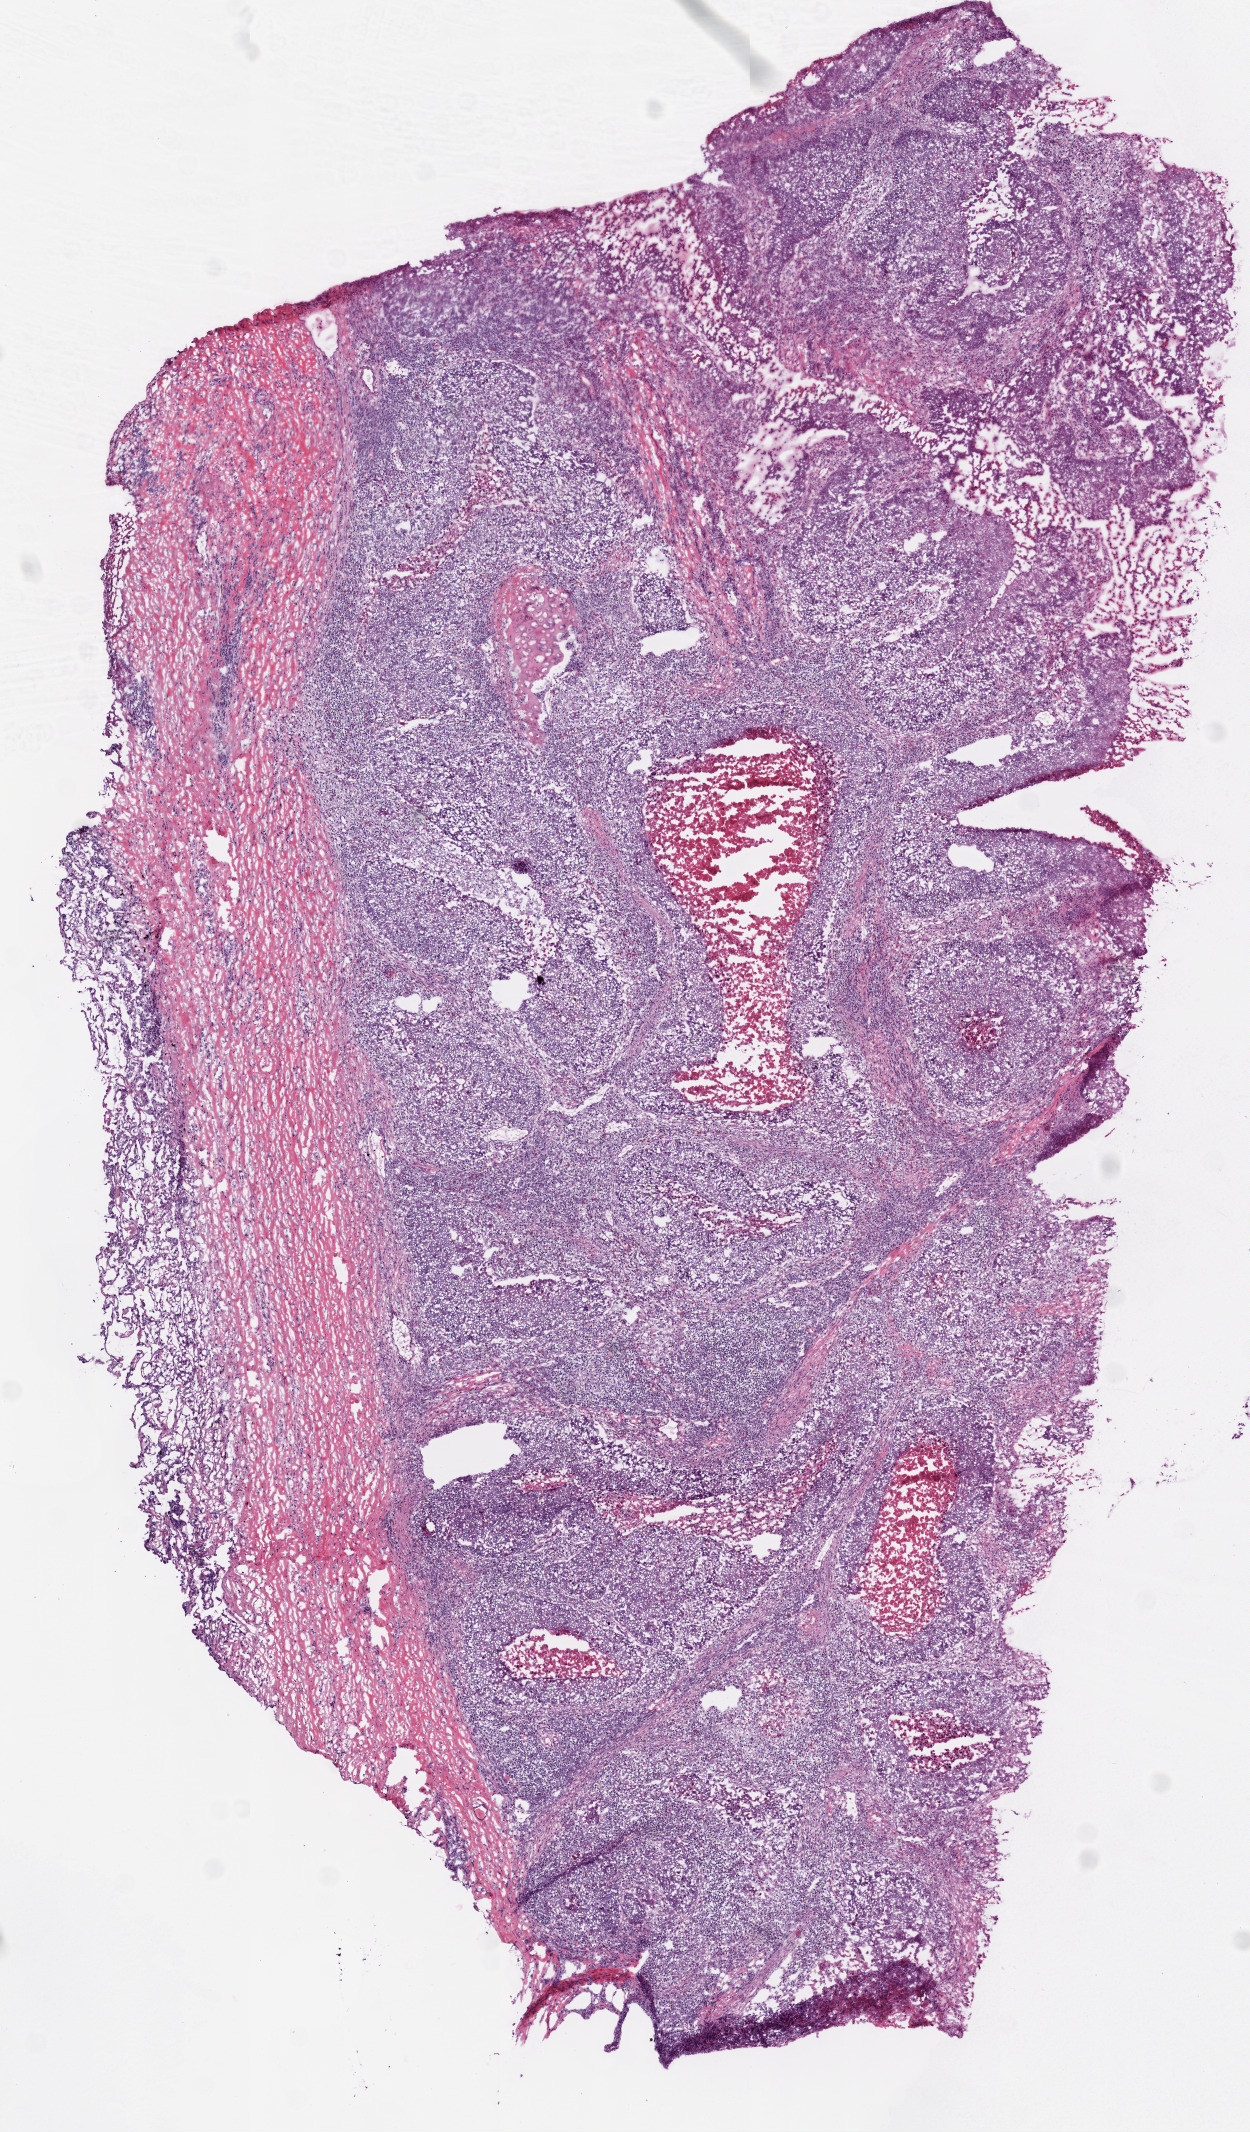
Digitized Hematoxylin and eosin (H&E) stained tissue section (whole slide), shown as a low-resolution overview of the whole scanned area (about 5.0 x 8.6 mm, slide scanned at 20x). Frozen section. Lung, primary tumour sample. Male, age 57 years at initial diagnosis. Slide review estimates, as recorded: tumour cells 70%, tumour nuclei 75%.
Pathologic diagnosis: Squamous cell carcinoma, NOS (upper lobe, lung).